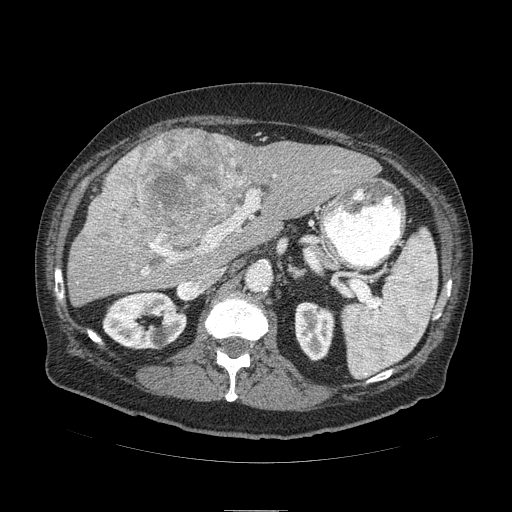
Contrast-enhanced abdominal CT (liver protocol), one axial slice. Reconstruction kernel STANDARD. 120 kVp. Soft-tissue window (W 400 / L 40 HU). 512 × 512 image matrix, field of view 440 × 440 mm. Case-level facts recorded for this patient, not image findings: diagnosis: hepatocellular carcinoma (patient treated with transarterial chemoembolisation; whether this scan precedes or follows treatment is not stated here); TNM stage (as recorded): Stage-IIIA; Child-Pugh class: B; tumour differentiation: well differentiated.
Annotated regions visible in this slice (semi-automatic segmentation, software-assisted and operator-edited):
- liver parenchyma outside the tumour (the mass and vessels are separate outlines, so this box may not span the whole liver): bounding box <66,134,380,306> (left, top, right, bottom; pixels)
- mass: <85,129,252,265>
- liver vessels: <131,159,276,276>